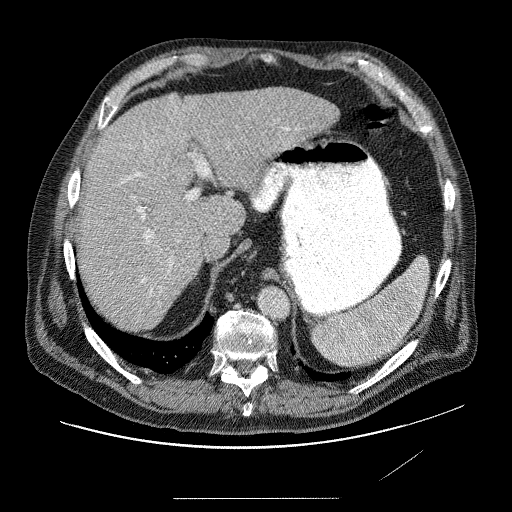
Contrast-enhanced abdominal CT (liver protocol), one axial slice. Position 56 of 89 along the scan axis. Reconstruction kernel STANDARD. 120 kVp. Soft-tissue window (W 400 / L 40 HU). 512 × 512 image matrix, field of view 420 × 420 mm. From the clinical record (not read from this slice): diagnosis: hepatocellular carcinoma (patient treated with transarterial chemoembolisation; whether this scan precedes or follows treatment is not stated here); TNM stage (as recorded): Stage-IVA; Child-Pugh class: A; tumour differentiation: moderately differentiated; tumour nodularity: multinodular.
Outlined on this slice (semi-automatically segmented with operator editing):
- abdominal aorta: bounding box (x1, y1, x2, y2) in pixels: (258, 288, 290, 318)
- liver parenchyma outside the tumour (the mass and vessels are separate outlines, so this box may not span the whole liver): (80, 86, 344, 314)
- mass: (143, 98, 272, 213)
- liver vessels: (101, 105, 294, 295)